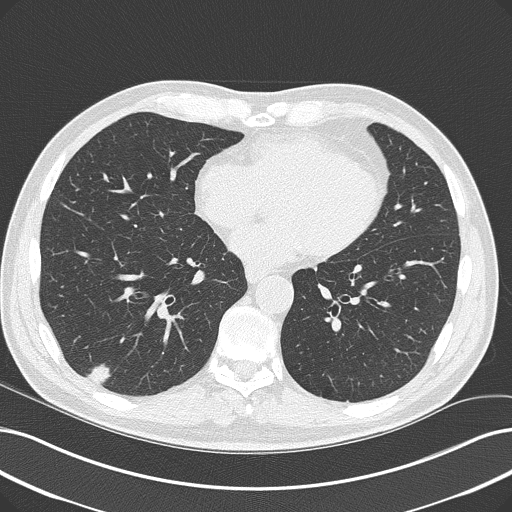
Low-dose screening chest CT, one axial slice. Reconstruction kernel B50f. 120 kVp. Lung window (W 1500 / L -600 HU). 2 mm slice thickness. 512 × 512 image matrix, field of view 366 × 366 mm.
Structures marked on this image (expert manual segmentation):
- lesion 1 (tumor, lower lobe of right lung): box from (x=87, y=364) to (x=111, y=384) px